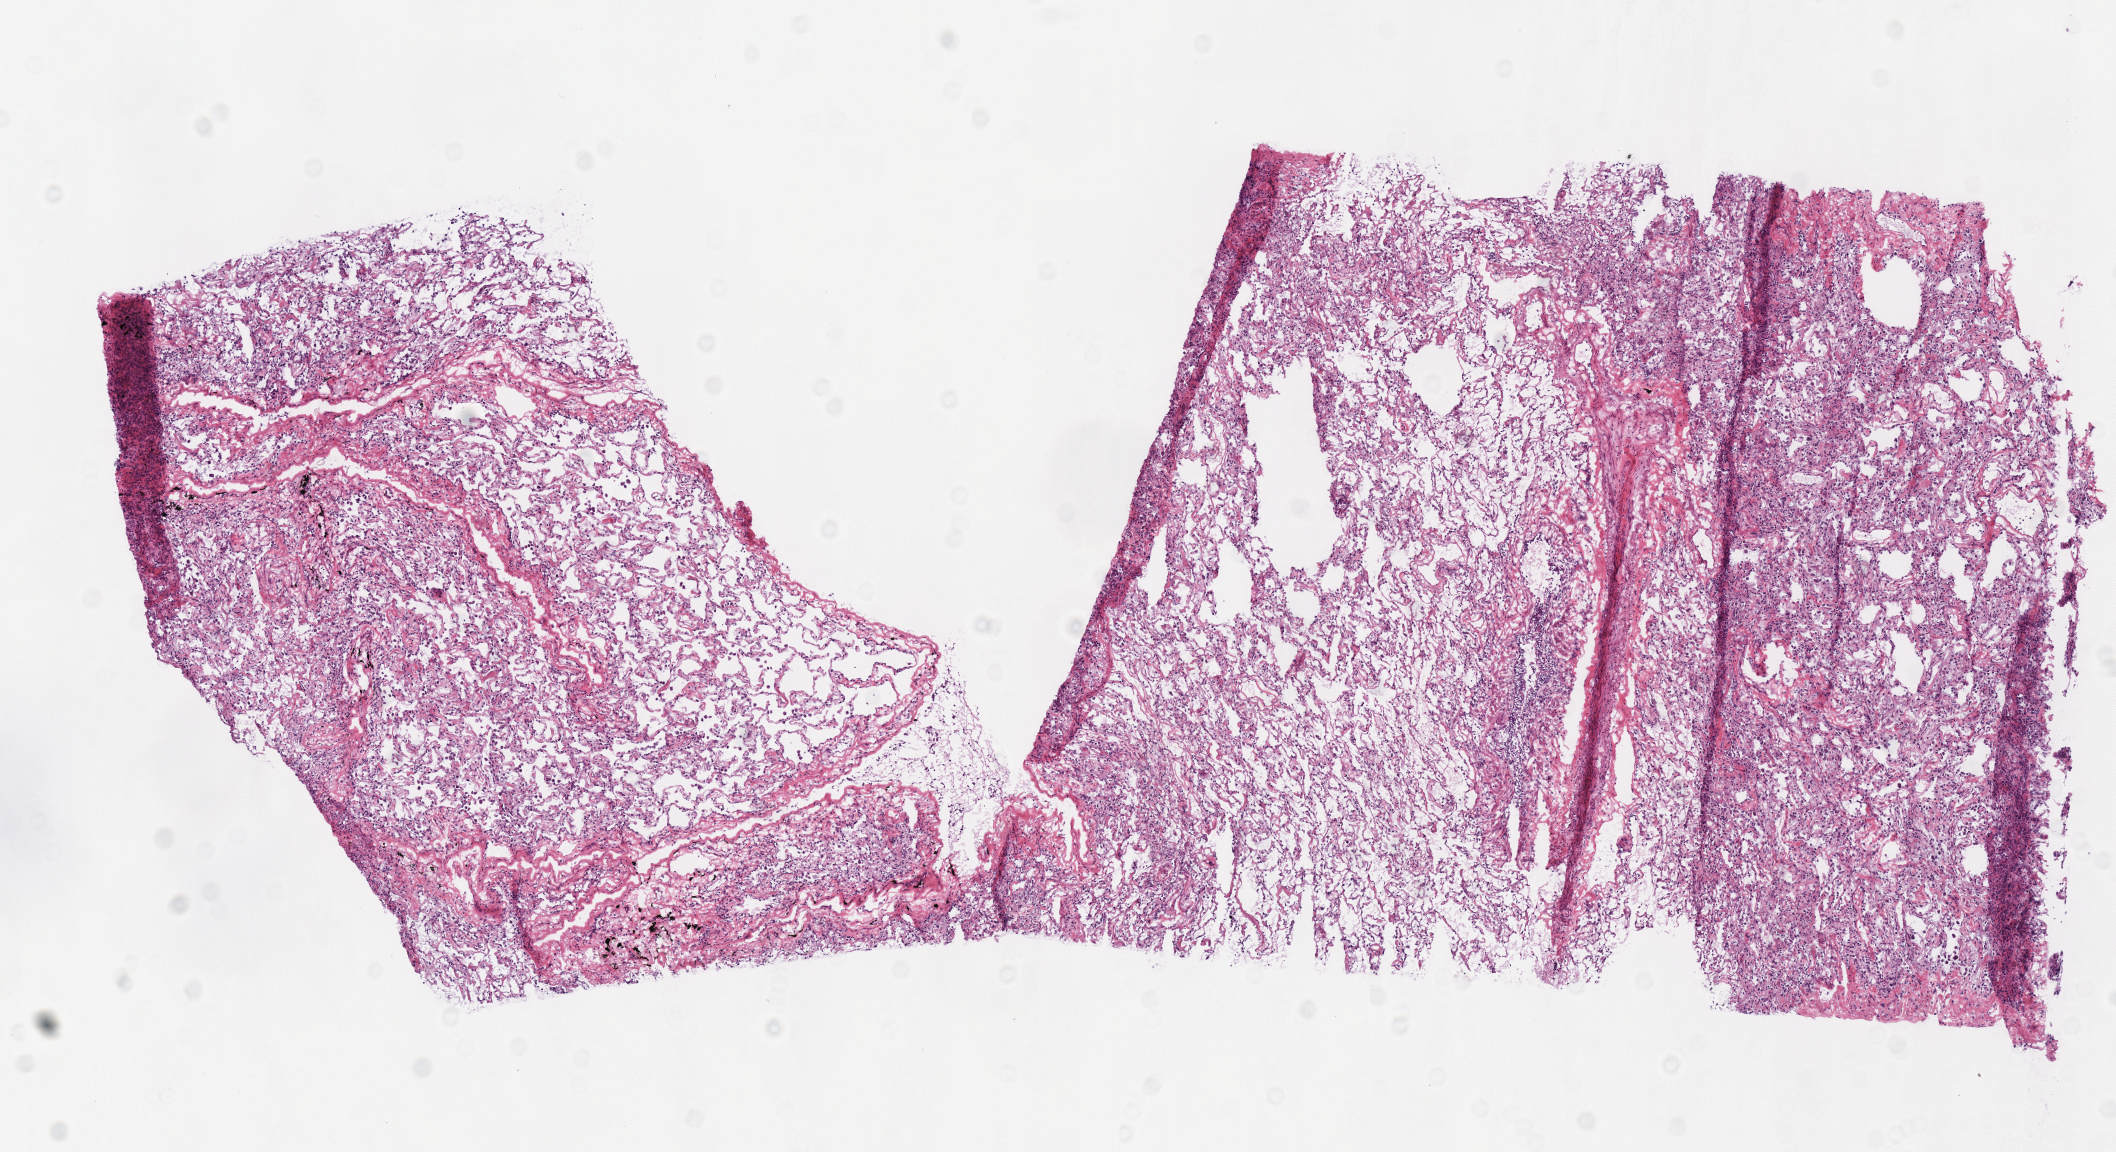
H&E-stained whole-slide image, shown as a low-resolution overview of the whole scanned area (about 8.3 x 4.5 mm, acquisition: 40x scan); frozen section from the top of the tissue portion; sample: solid tissue normal (non-tumour tissue), lung. Female patient; age at initial diagnosis 68 years.
This section: solid tissue normal sample (biorepository sample class). Patient diagnosis: Adenocarcinoma, NOS.